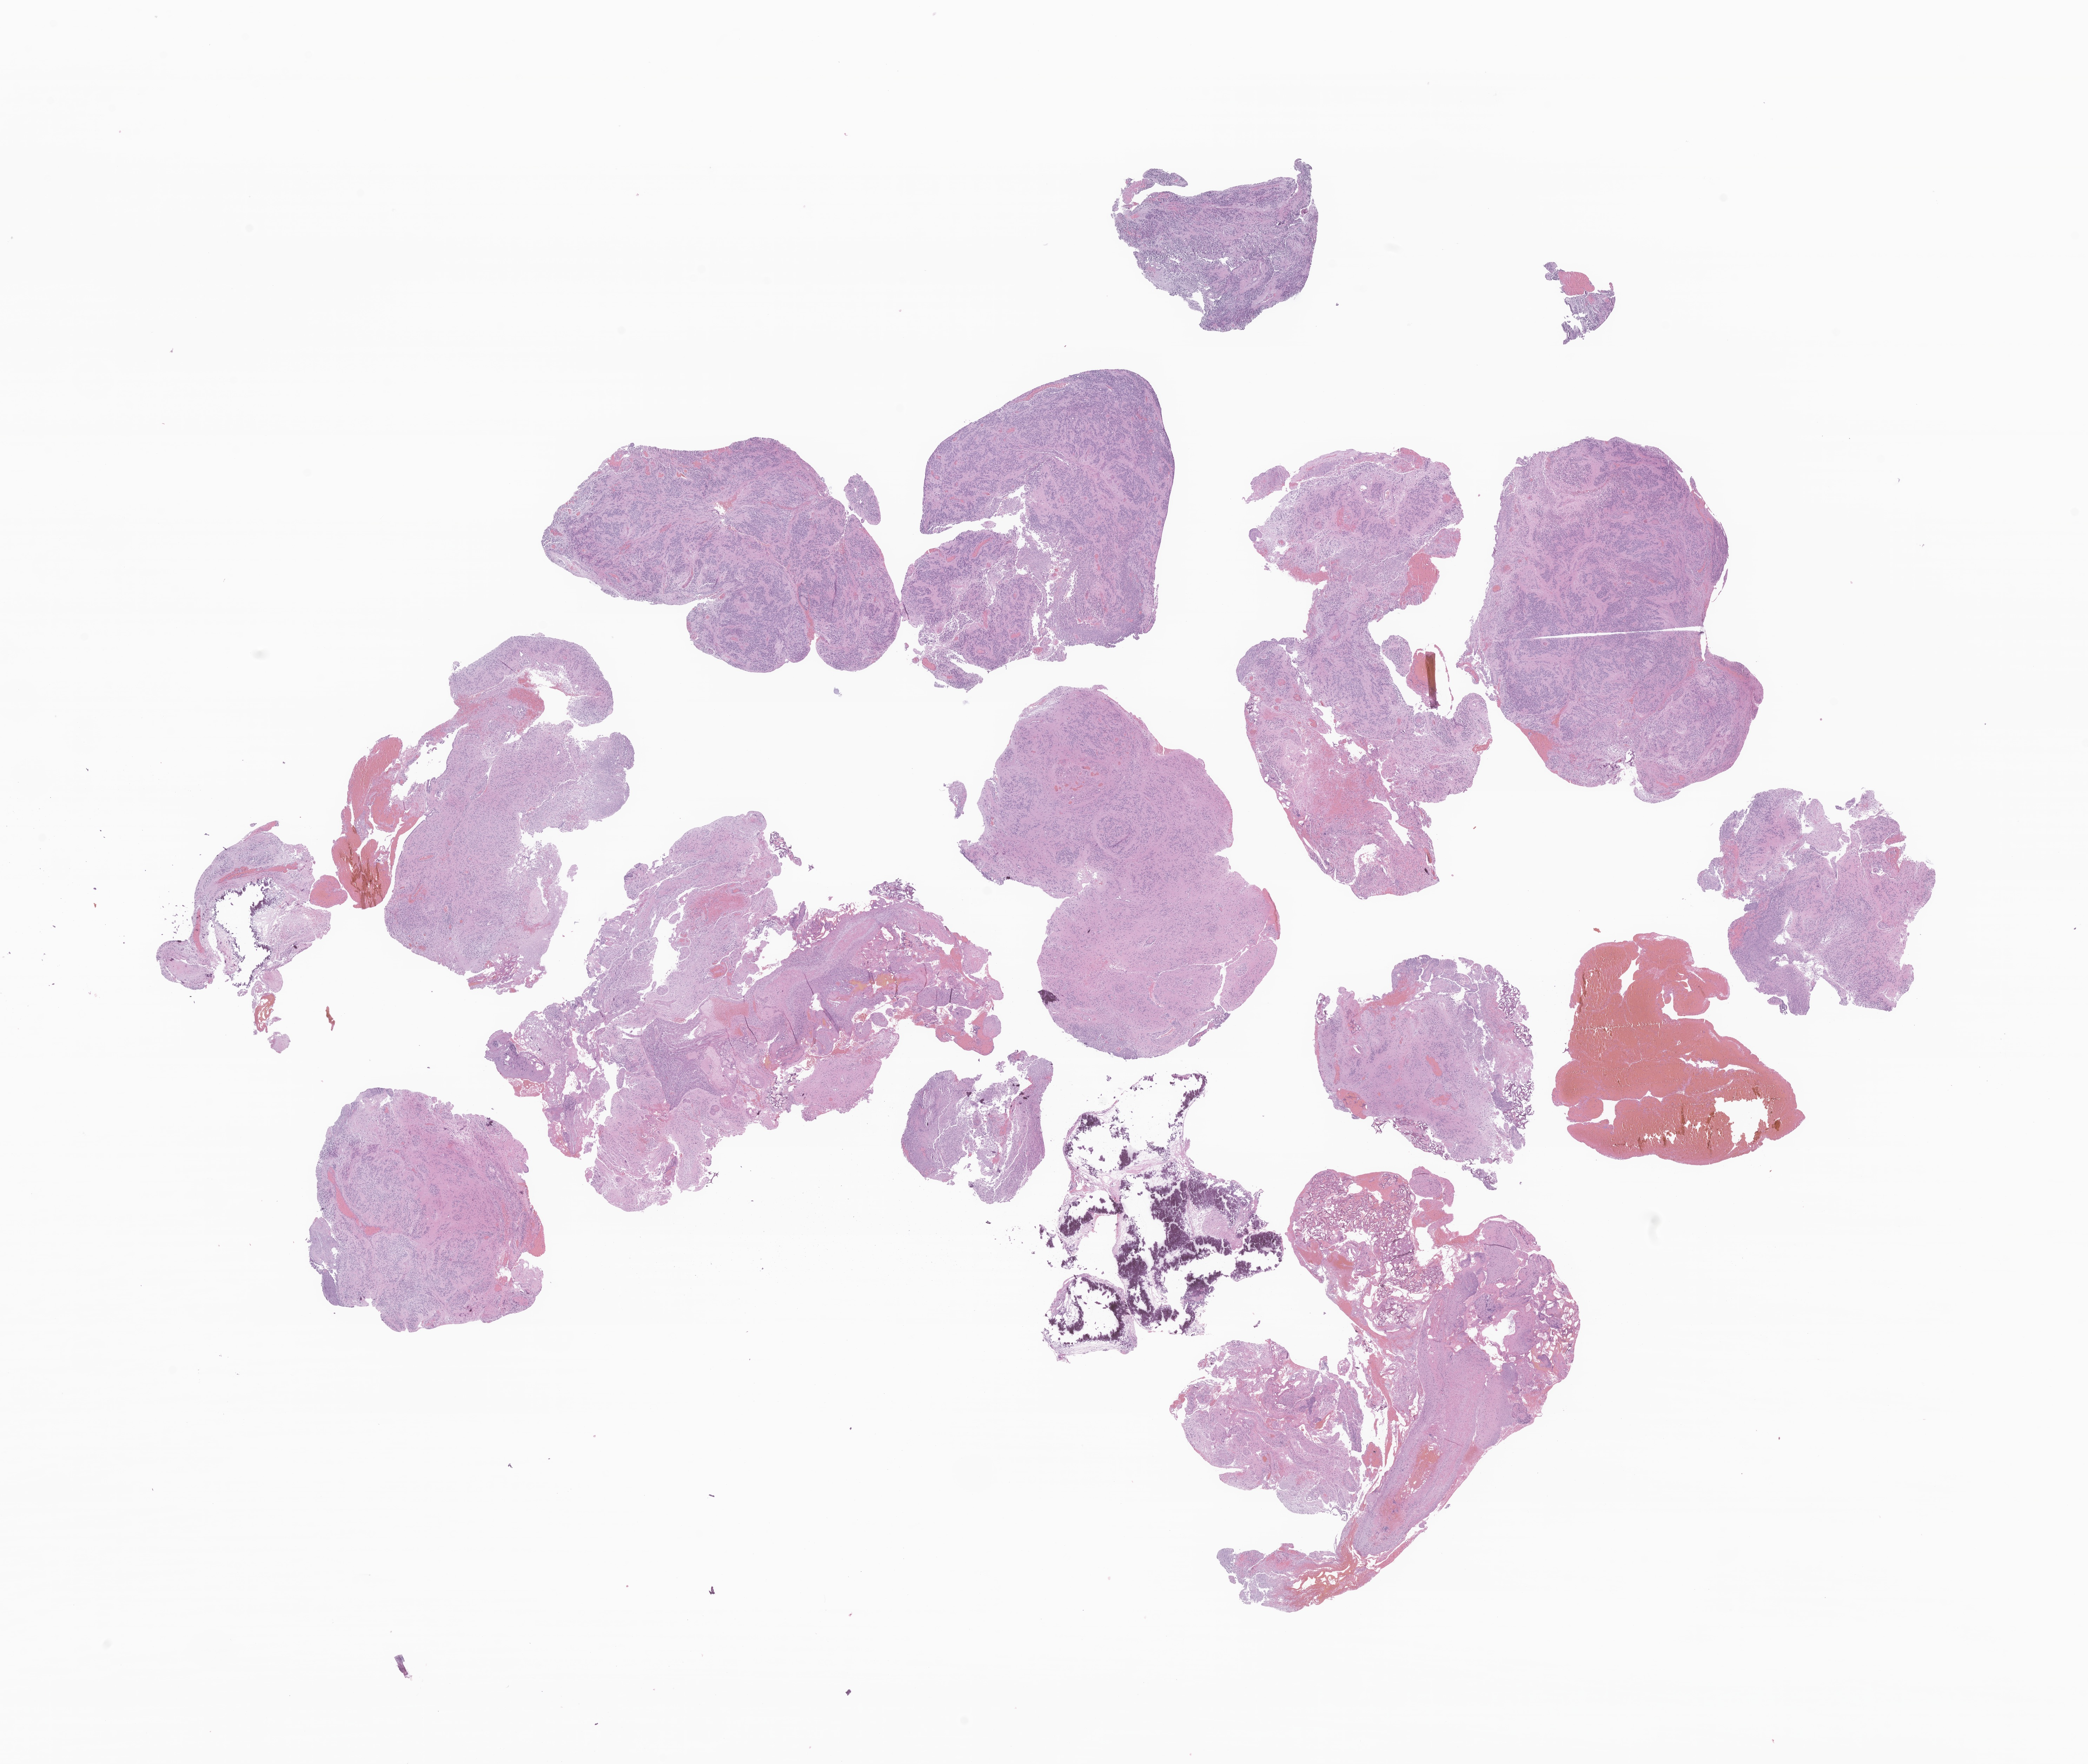
Digitized haematoxylin and eosin-stained section of tumor tissue from the cerebellum, whole scanned area (about 25.1 x 21.2 mm) shown as a low-resolution overview, formalin-fixed paraffin-embedded section. Patient female; age 85 months (7 years 1 month).
Diagnosis: Ependymoma, NOS.